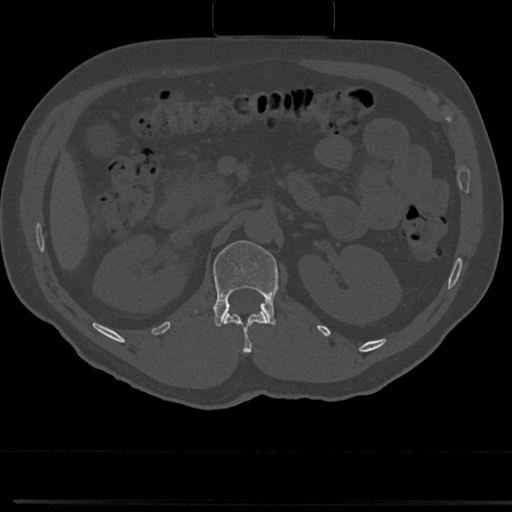
CT including the spine, one axial slice; position 102 of 817 along the scan axis; reconstruction kernel Br40s/3; 120 kVp; bone window (W 1800 / L 400 HU); 0.5 mm slice thickness; 512 × 512 image matrix, field of view 355 × 355 mm. Patient: male, 61 years. From the clinical record (not read from this slice): primary cancer: prostate.
Outlined on this slice (semi-automatically segmented with operator editing):
- L1 vertebra: box from (x=191, y=240) to (x=278, y=327) px
- T12 vertebra: (x=225, y=312)–(x=268, y=351)